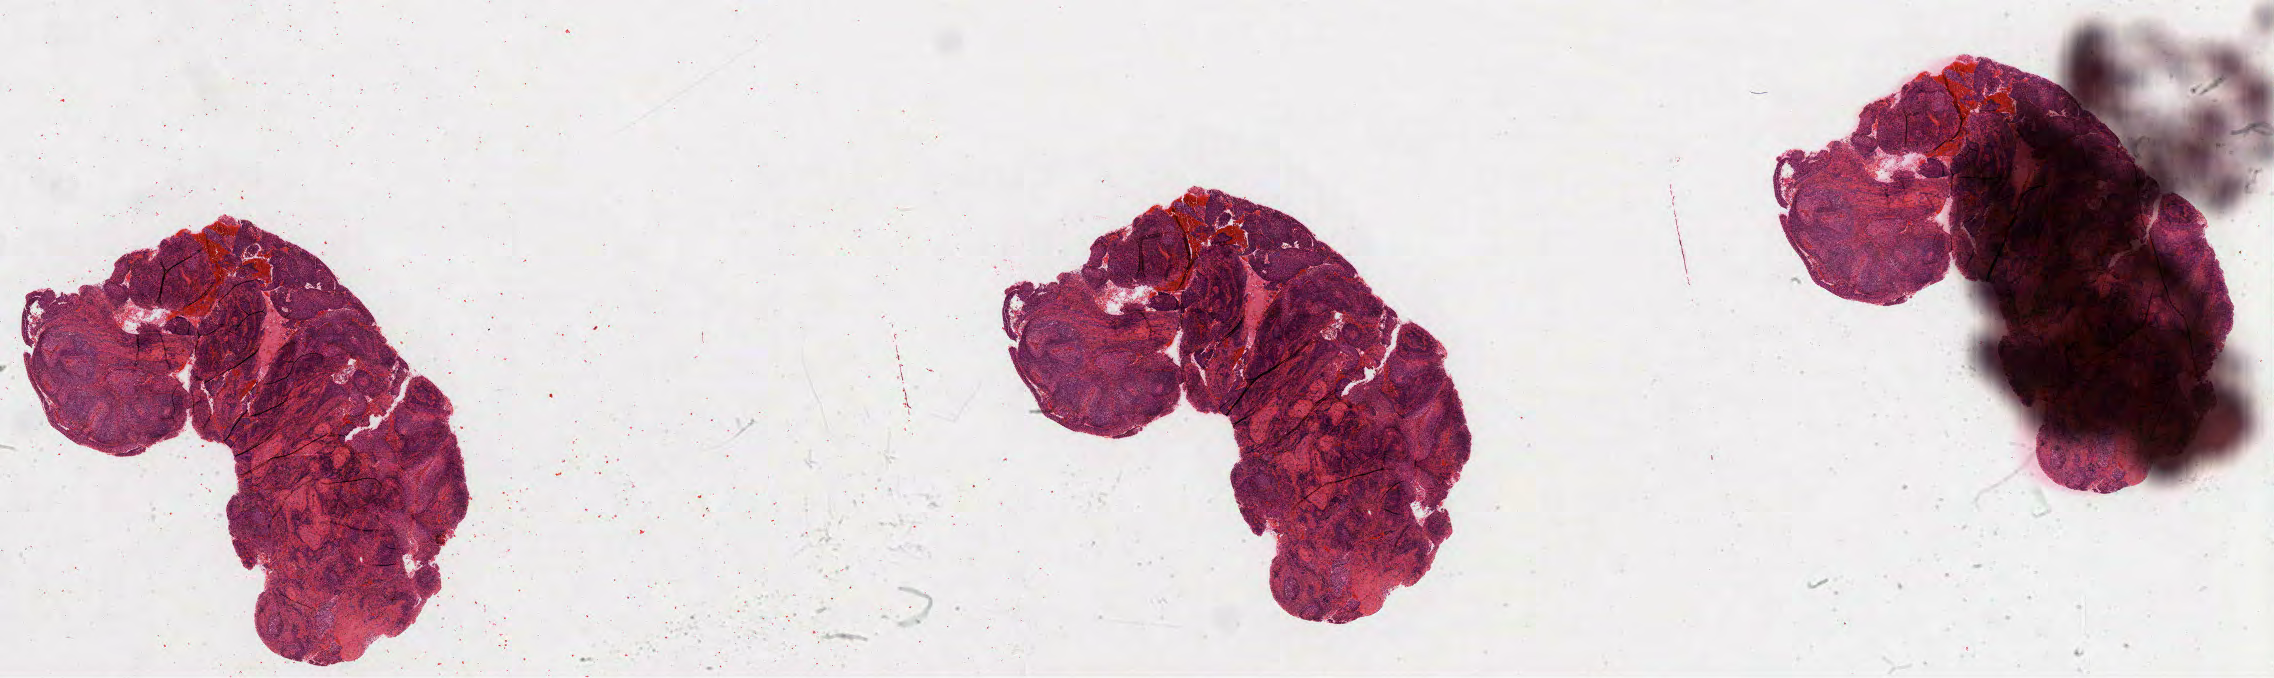
Whole-slide histology image, Hematoxylin and eosin (H&E) stained — a low-resolution overview of the entire scanned area, about 36.6 x 10.9 mm (acquisition: 40x scan), FFPE section, sample: primary tumour, cervix. Female, age 48 years at initial diagnosis.
FIGO stage: IIIB. Diagnosis: Squamous cell carcinoma, large cell, nonkeratinizing, NOS.